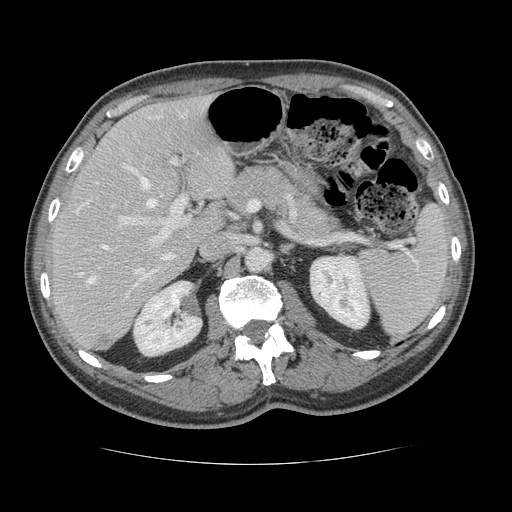
Contrast-enhanced abdominal CT, one axial slice; position 78 of 134 along the scan axis; reconstruction kernel STANDARD; 120 kVp; intravenous contrast given; soft-tissue window (W 400 / L 40 HU); 2.5 mm slice thickness; 512 × 512 image matrix. Male patient, age 68 years. Case-level facts recorded for this patient, not image findings: diagnosis: colorectal cancer liver metastases, imaged before liver resection; multiple liver metastases: yes; largest metastasis: 2.2 cm; disease in both lobes: no.
Outlined on this slice (outlined manually by an expert reader):
- hepatic veins: bounding box [x1, y1, x2, y2] px = [77, 117, 158, 284]
- liver: [50, 97, 234, 350]
- planned liver remnant (the part of the liver to remain after resection): [49, 97, 234, 339]
- portal vein (with intrahepatic branches): [119, 113, 188, 279]
- liver metastasis: [96, 335, 115, 350]